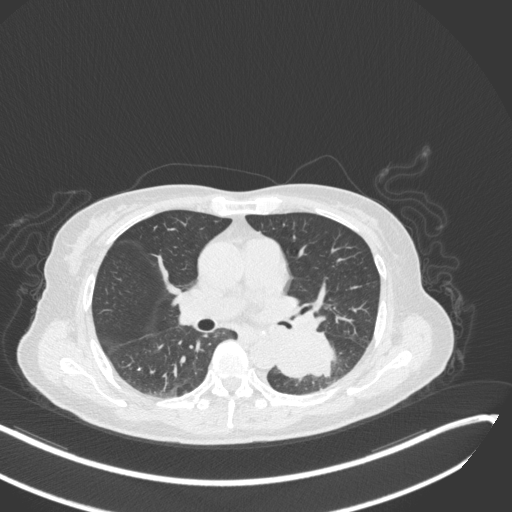
Chest CT, one axial slice. Slice 153 of 342 in the series (ordered by position). Reconstruction kernel B31f. 120 kVp. Lung window (W 1500 / L -600 HU). 1 mm slice thickness. 512 × 512 image matrix, field of view 400 × 400 mm. Patient: female, 64 years. Case-level facts recorded for this patient, not image findings: clinical TNM (as recorded): T3 N1 M1.
Structures marked on this image (bounding box drawn by a radiologist):
- lung tumour (recorded histology: small cell carcinoma): bounding box [x1, y1, x2, y2] px = [276, 332, 341, 386]